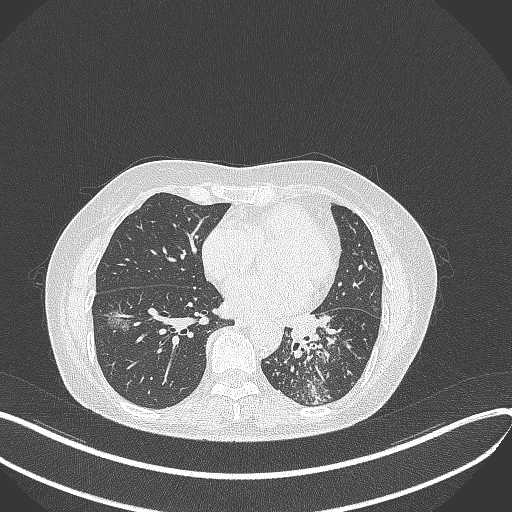
Chest CT, one axial slice; position 167 of 429 along the scan axis; reconstruction kernel B70f; 100 kVp; lung window (W 1500 / L -600 HU); 1 mm slice thickness; 512 × 512 image matrix, field of view 400 × 400 mm. Patient: female, 63 years. From the clinical record (not read from this slice): clinical TNM (as recorded): T1b N0 M0.
Outlined on this slice (bounding box drawn by a radiologist):
- lung tumour (recorded histology: adenocarcinoma): bounding box (x1, y1, x2, y2) in pixels: (279, 304, 319, 347)